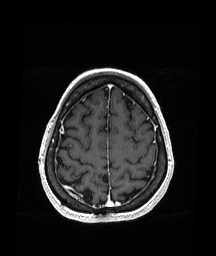
Brain MRI from a brain-tumour surgery series, one axial slice. T1-weighted post-contrast. 1.05 mm slice thickness. 216 × 256 image matrix, field of view 211 × 250 mm. From the clinical record (not read from this slice): histopathology: Oligodendroglioma; WHO grade: 2; IDH mutation: yes.
Outlined on this slice (expert manual segmentation):
- previous resection cavity: bounding box <94,173,109,181> (left, top, right, bottom; pixels)